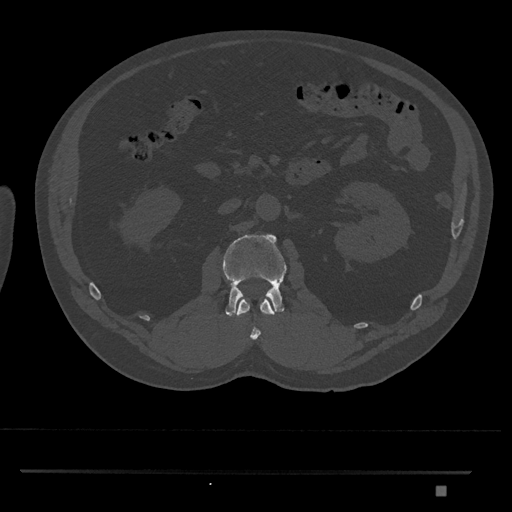
CT including the spine, one axial slice; position 779 of 1134 along the scan axis; reconstruction kernel Br40s/3; 120 kVp; bone window (W 1800 / L 400 HU); 512 × 512 image matrix, field of view 429 × 429 mm. Male patient, age 65 years. From the clinical record (not read from this slice): primary cancer: prostate.
Outlined on this slice (semi-automatically segmented with operator editing):
- L1 vertebra: bounding box <236,298,275,340> (left, top, right, bottom; pixels)
- L2 vertebra: <222,233,287,317>